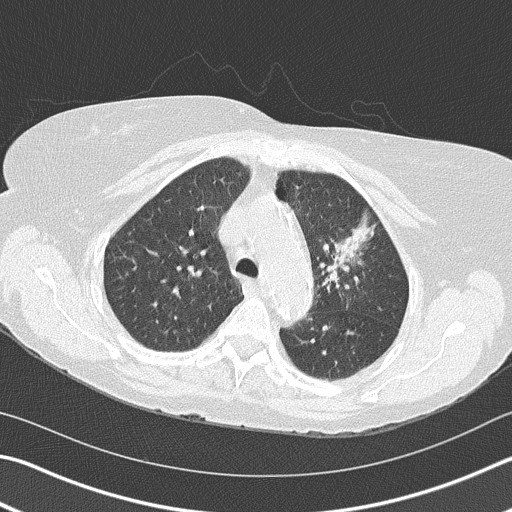
Chest CT (low-dose screening protocol), one axial image, second annual screen, lung window (W 1500 / L -600 HU), lung (sharp) reconstruction kernel (B50f), slice 116 of 153 in the series. Female, age 68 years at enrolment. Former smoker at enrolment.
- Expert reader's lesion annotation, bounding box [x1, y1, x2, y2] px = [293, 202, 389, 313].
- Screening reader's record for this exam (one nodule recorded; not confirmed to be the boxed lesion): non-calcified nodule or mass ≥4 mm, left upper lobe, 4 × 2 mm, spiculated (stellate) margins, soft tissue attenuation, pre-existing on the prior screen: yes; interval growth: yes.
- Lung cancer was diagnosed 392 days after this screen (after the third annual screen): adenocarcinoma, NOS, left upper lobe, poorly differentiated (G3), stage IB (AJCC 6th edition), 50 mm at pathology.